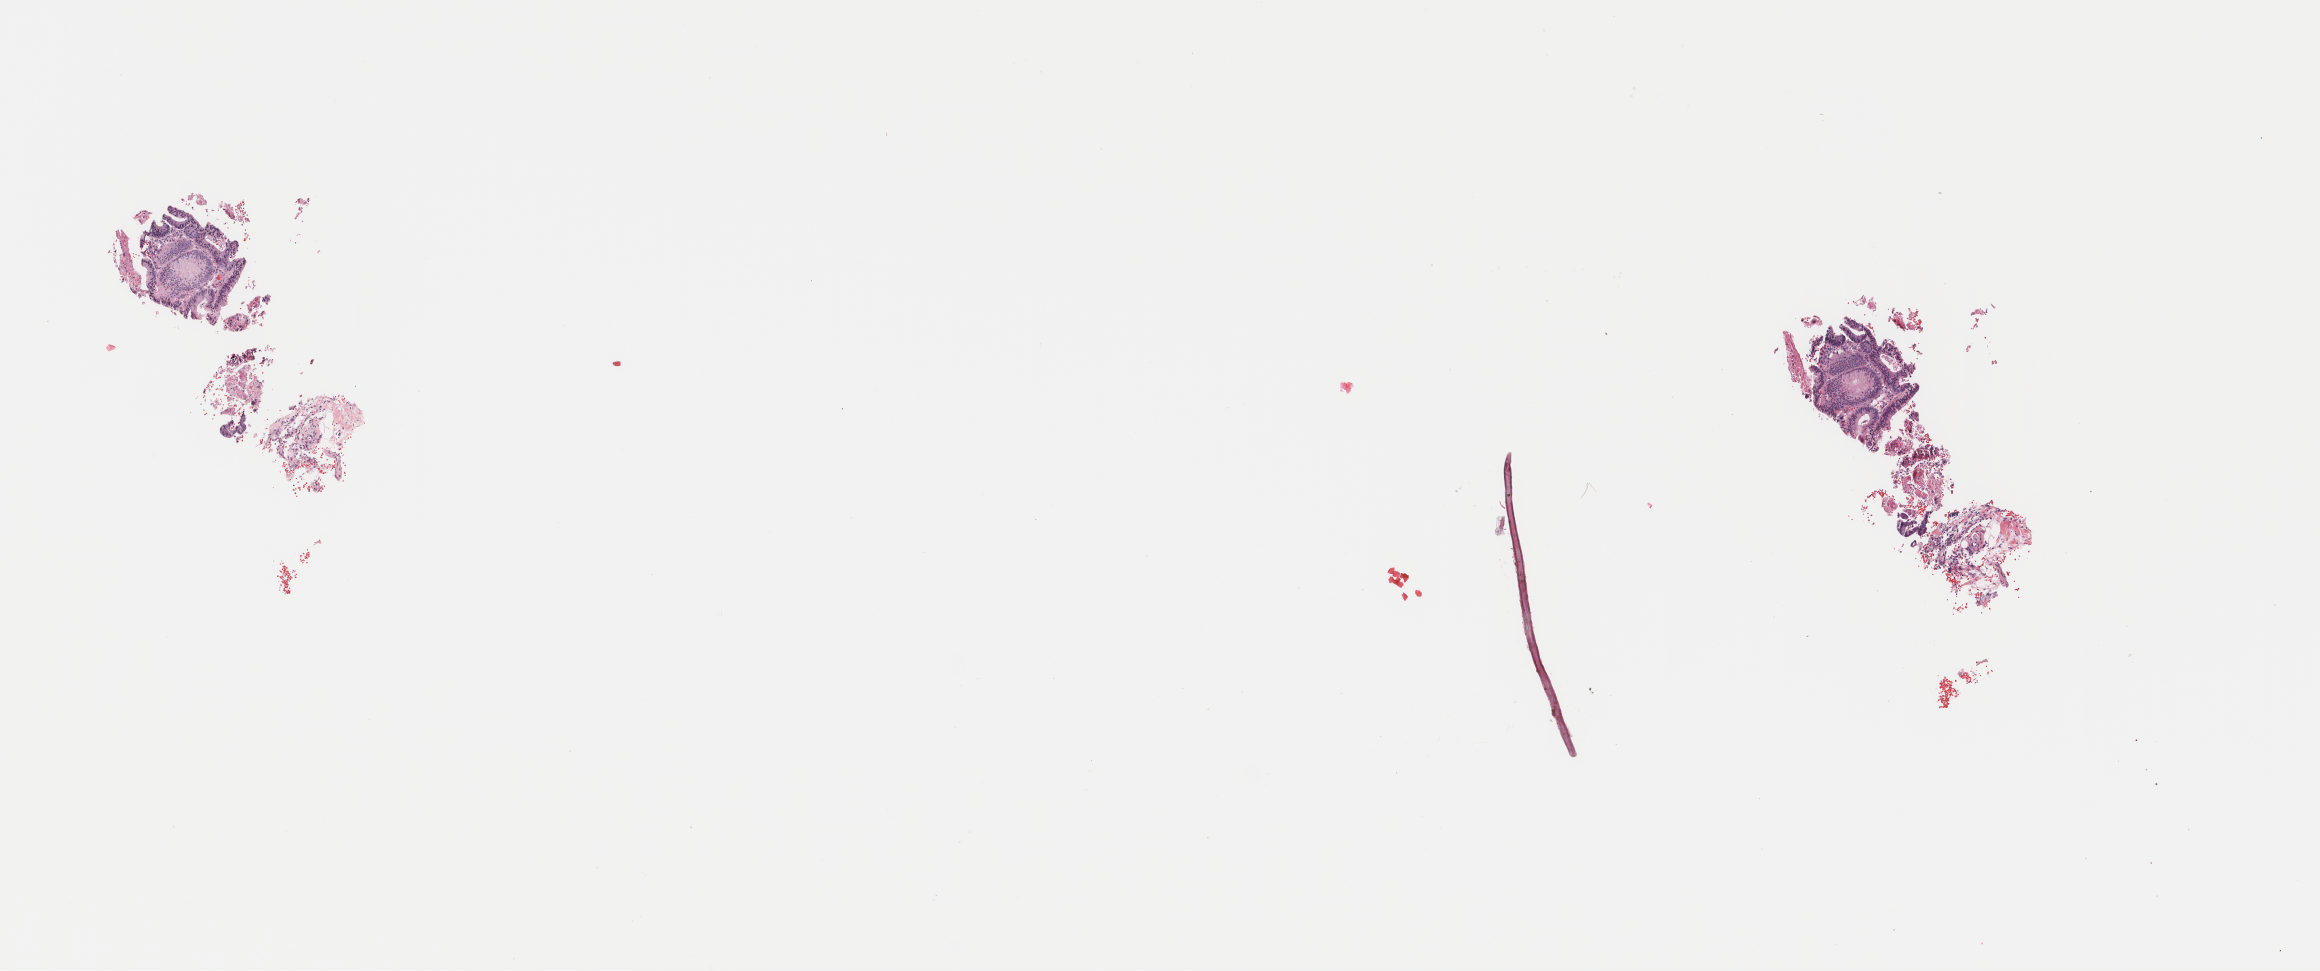
Digitized H&E tissue section (whole slide), low-resolution overview of the scanned area, about 9.2 x 3.9 mm (slide scanned at 40x), frozen section, colon, primary tumour sample. Male, age 74 years at initial diagnosis. Composition of this section per pathologist review: tumour cells 80%, tumour nuclei 85%, normal cells 0%, stromal cells 15%, necrosis 5%. Inflammatory infiltration, as recorded: lymphocyte infiltration 0%, monocyte infiltration 0%, neutrophil infiltration 0%.
Lymph nodes positive (case pathology): 0 of 16 examined. Pathologic diagnosis: Adenocarcinoma, NOS (sigmoid colon). AJCC pathologic stage: I (7th edition).